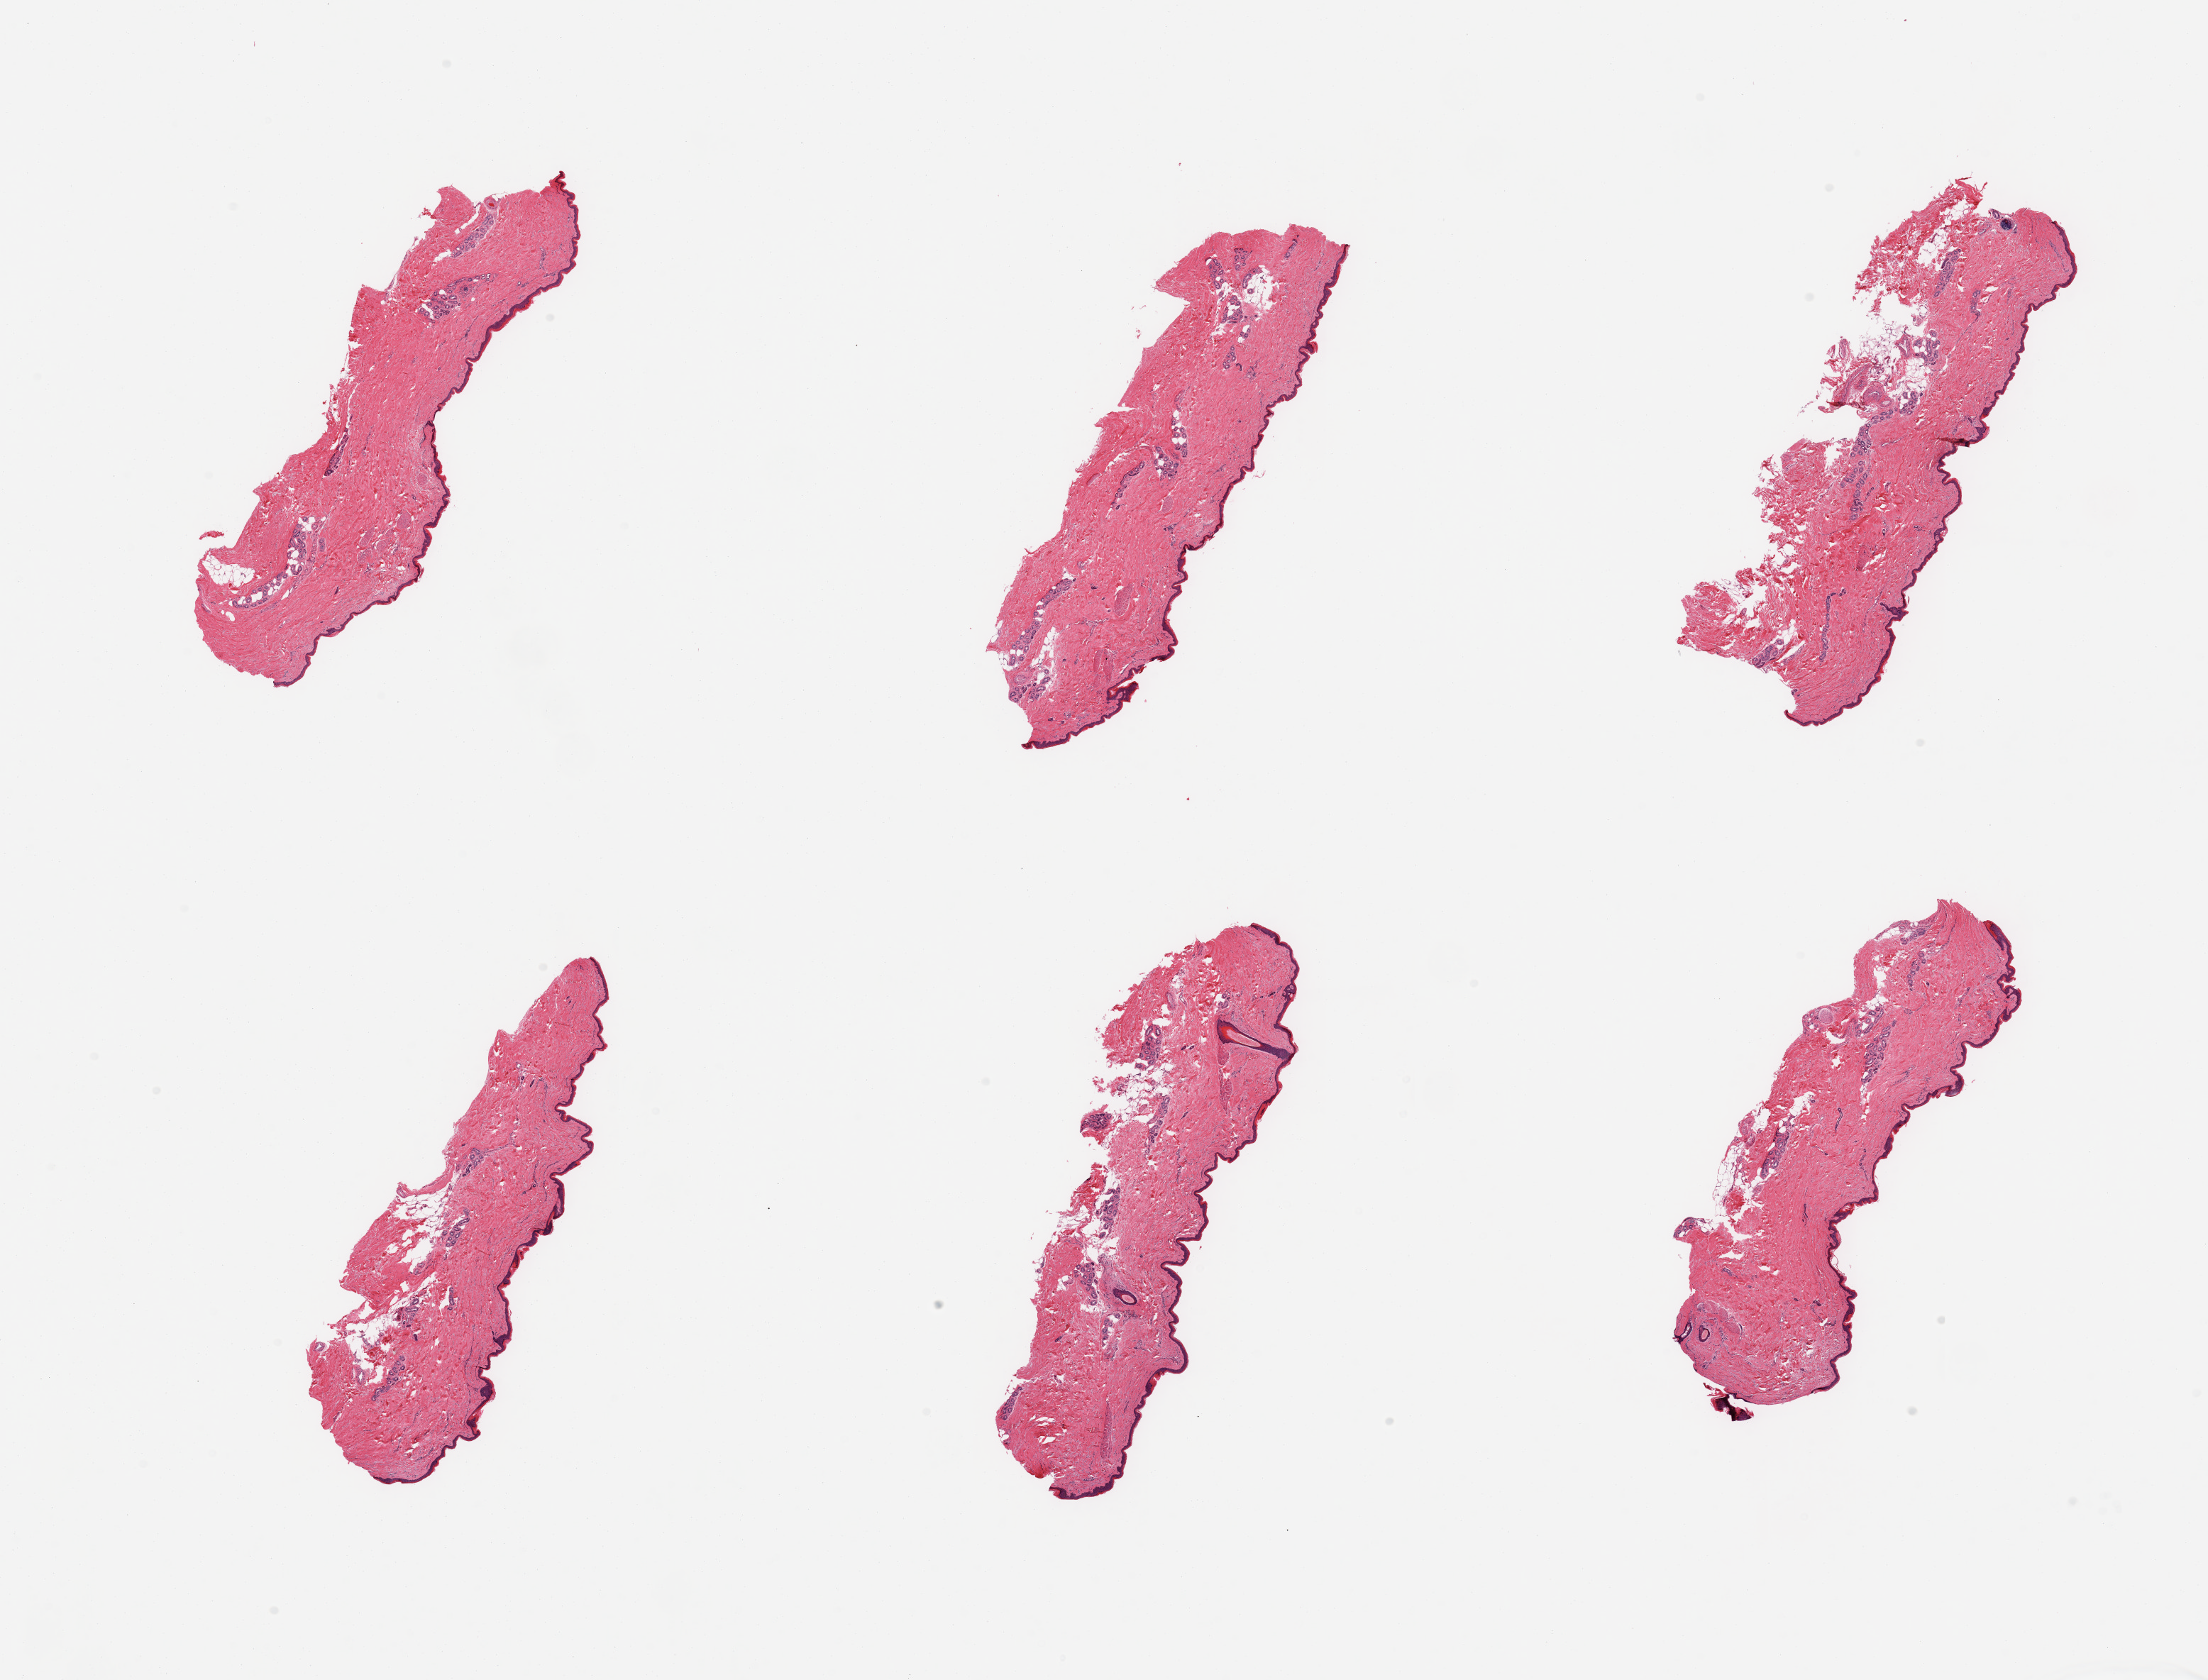
H&E whole-slide image — low-resolution overview of the scanned area, about 24.6 x 18.7 mm (acquisition: 20x scan); PAXgene-fixed paraffin-embedded (PFPE) section; target tissue: skin of lower leg; donor tissue sample. Donor: male.
Pathologist's review note for this sample: 6 pieces; 1% to 5% dermal fat; ~34 micron thick epidermis.